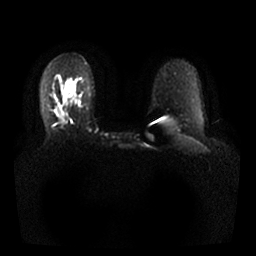
Breast MRI, one axial slice; position 20 of 25 along the scan axis; diffusion-weighted series; image 2 of 4 stored at this slice position (different b-values; order by instance number); 1.5 T; 4 mm slice thickness; 256 × 256 image matrix, field of view 350 × 350 mm. Female patient.
Structures marked on this image (outlined manually by an expert reader):
- tumour on diffusion-weighted imaging: bounding box [x1, y1, x2, y2] px = [58, 109, 63, 117]